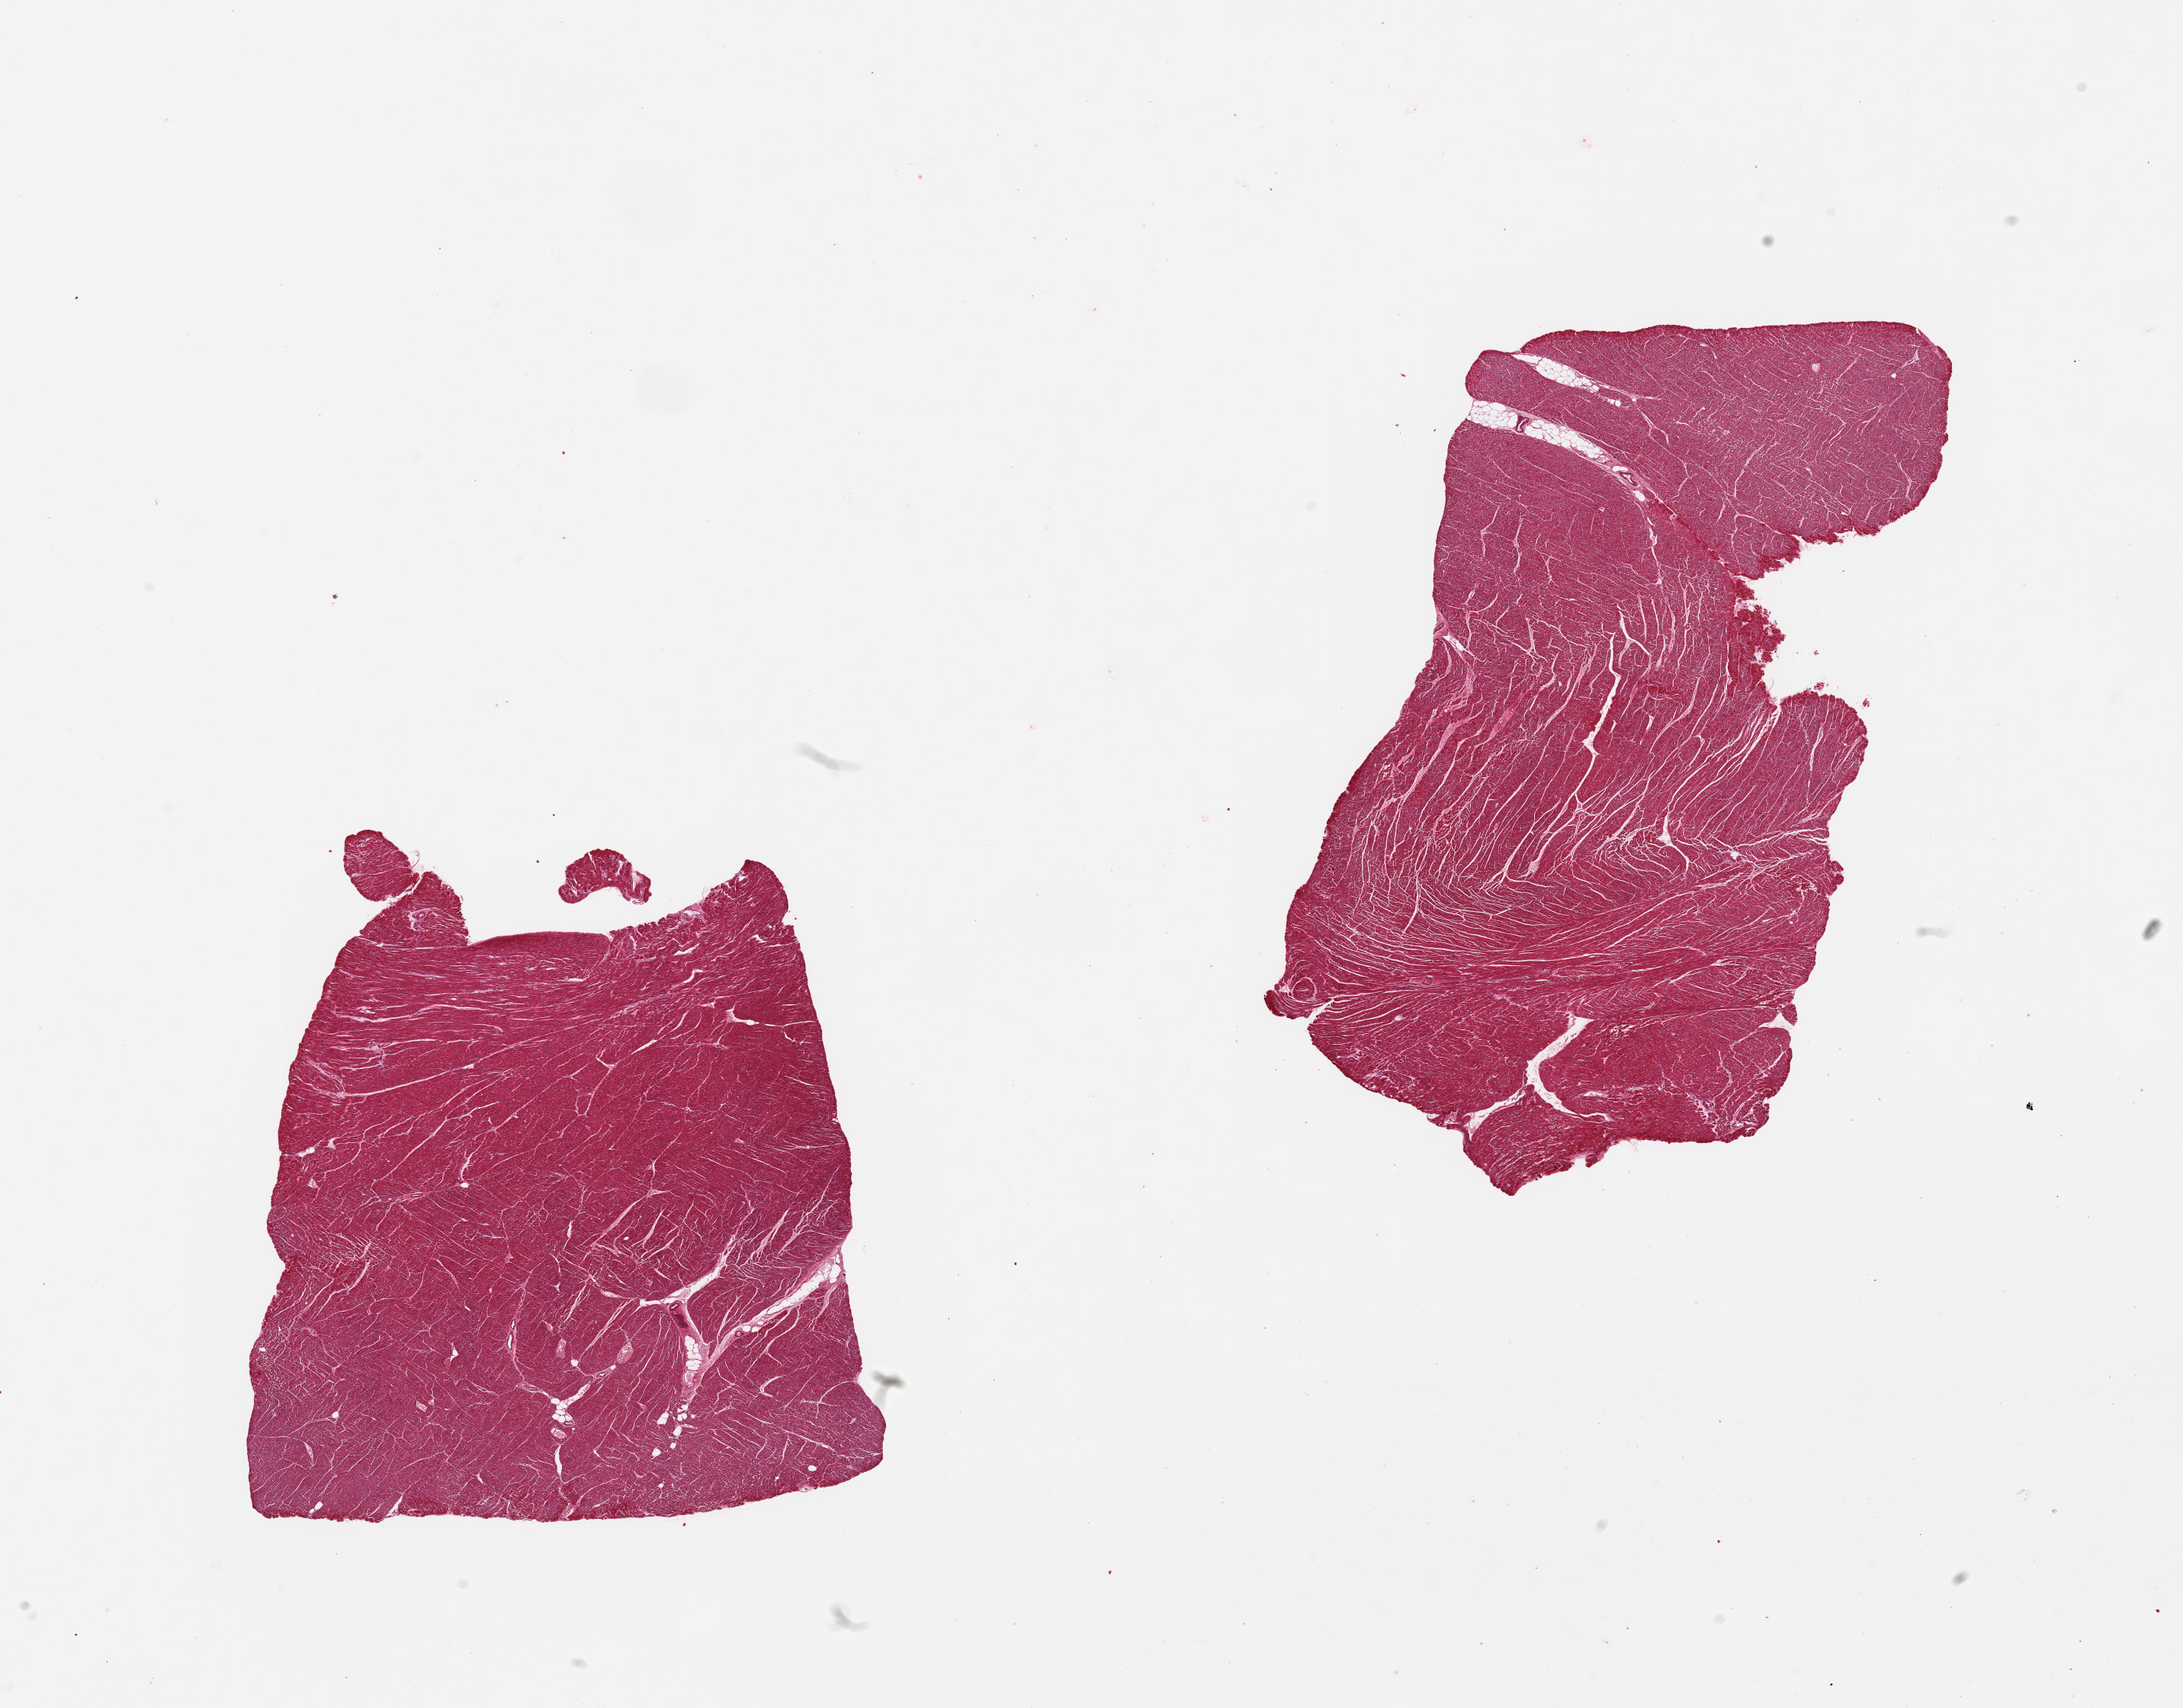
Whole-slide image, H&E stain, shown as a low-resolution overview of the whole scanned area (about 22.6 x 17.7 mm); PAXgene-fixed, paraffin-embedded tissue; sampled site (target tissue): heart; tissue donor sample. Female donor.
* review note (as recorded): 2 pieces; minimal internal fat